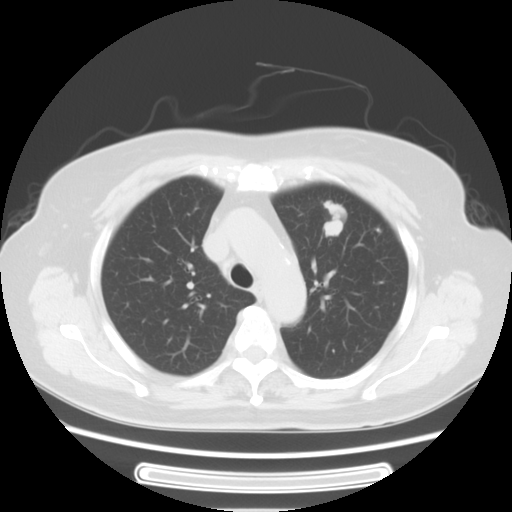
Chest CT, one axial slice; position 44 of 57 along the scan axis; reconstruction kernel STANDARD; 120 kVp; lung window (W 1500 / L -600 HU); 5 mm slice thickness; 512 × 512 image matrix, field of view 363 × 363 mm. Female patient, age 77 years. Case-level facts recorded for this patient, not image findings: clinical TNM (as recorded): T1c N3 M0.
Structures marked on this image (rectangle marked by the reading radiologist):
- lung tumour (recorded histology: adenocarcinoma): bounding box [x1, y1, x2, y2] px = [312, 189, 354, 252]